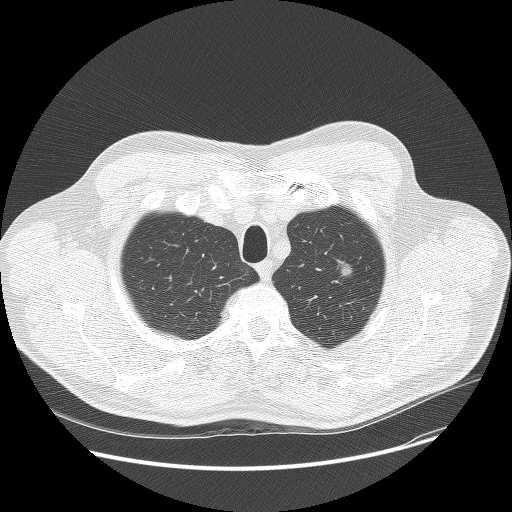
Low-dose screening chest CT, axial slice, baseline annual screen, lung window (W 1500 / L -600 HU), lung (sharp) reconstruction kernel (BONE), 120 kVp, 512 × 512 image matrix. Male, age 60 years at enrolment. Former smoker at enrolment.
• Lesion marked by an expert reader, bounding box <327,248,370,291> (left, top, right, bottom; pixels).
• The screening reader recorded 2 non-calcified nodules or masses ≥4 mm on this exam; which of them this box marks is not recorded.
• Participant outcome: lung cancer diagnosed 784 days after this screen (after the third annual screen) — bronchiolo-alveolar carcinoma, non-mucinous, left upper lobe, well differentiated (G1), stage IA (AJCC 6th edition), 16 mm at pathology.